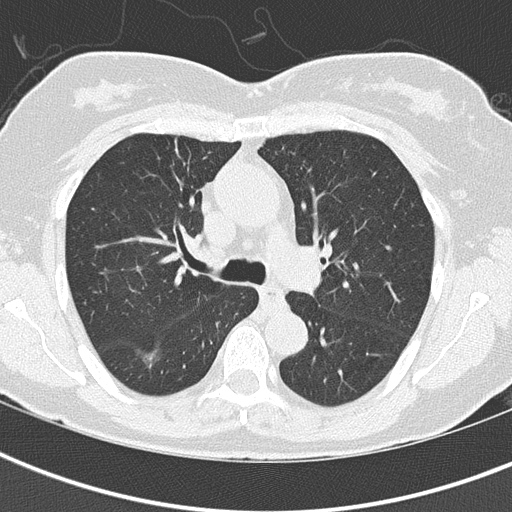
Chest CT (low-dose screening protocol), one axial image; baseline annual screen; lung window (W 1500 / L -600 HU); 512 × 512 image matrix. Female participant, aged 68 years at enrolment. Former smoker at enrolment.
Lesion marked by an expert reader, bounding box [x1, y1, x2, y2] px = [118, 325, 178, 379]. Screening reader's record for this exam (one nodule recorded; not confirmed to be the boxed lesion): non-calcified nodule or mass ≥4 mm, right lower lobe, 19 × 17 mm, spiculated (stellate) margins, ground glass attenuation. Official screen result: positive, change unspecified: nodule(s) >= 4 mm or enlarging nodule(s), mass(es), or other non-specific abnormalities suspicious for lung cancer.